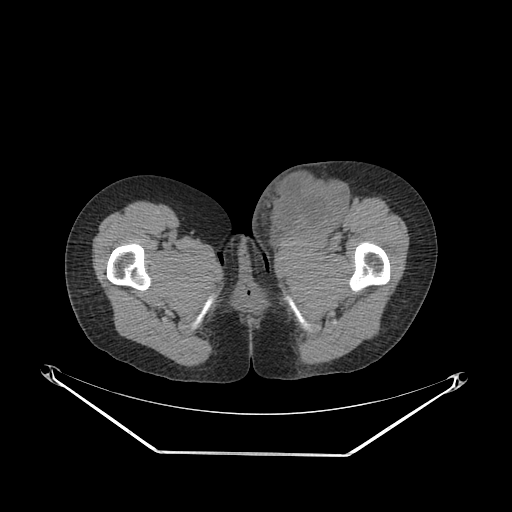
CT of an extremity soft-tissue mass (from a PET/CT study), one axial slice. Slice 51 of 267 in the series (ordered by position). Reconstruction kernel SOFT. Soft-tissue window (W 400 / L 40 HU). 3.75 mm slice thickness. 512 × 512 image matrix. Female patient. Case-level facts recorded for this patient, not image findings: histological type: leiomyosarcoma; grade: high; site of the primary tumour: groin.
Annotated regions visible in this slice (expert contour drawn on MRI and transferred to this co-registered scan by the dataset authors):
- gross tumour volume including surrounding oedema: bounding box <249,160,348,243> (left, top, right, bottom; pixels)
- gross tumour volume (mass): <272,171,348,238>